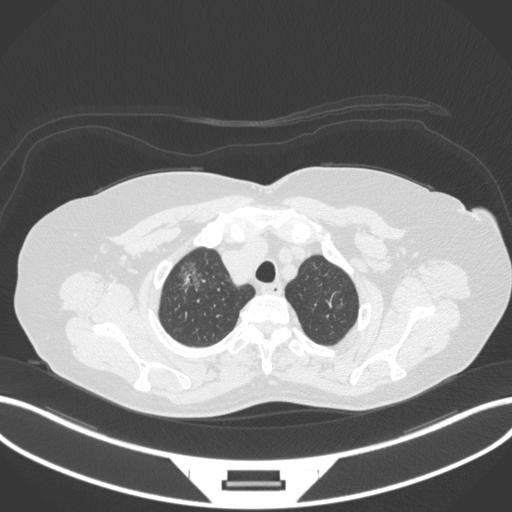
Chest CT, one axial slice. Position 305 of 365 along the scan axis. Reconstruction kernel B31f. 120 kVp. Lung window (W 1500 / L -600 HU). 1 mm slice thickness. 512 × 512 image matrix, field of view 400 × 400 mm. Female patient, age 62 years. Case-level facts recorded for this patient, not image findings: clinical TNM (as recorded): T1c N0 M0.
Structures marked on this image (bounding box drawn by a radiologist):
- lung tumour (recorded histology: adenocarcinoma): bounding box (x1, y1, x2, y2) in pixels: (176, 259, 209, 298)